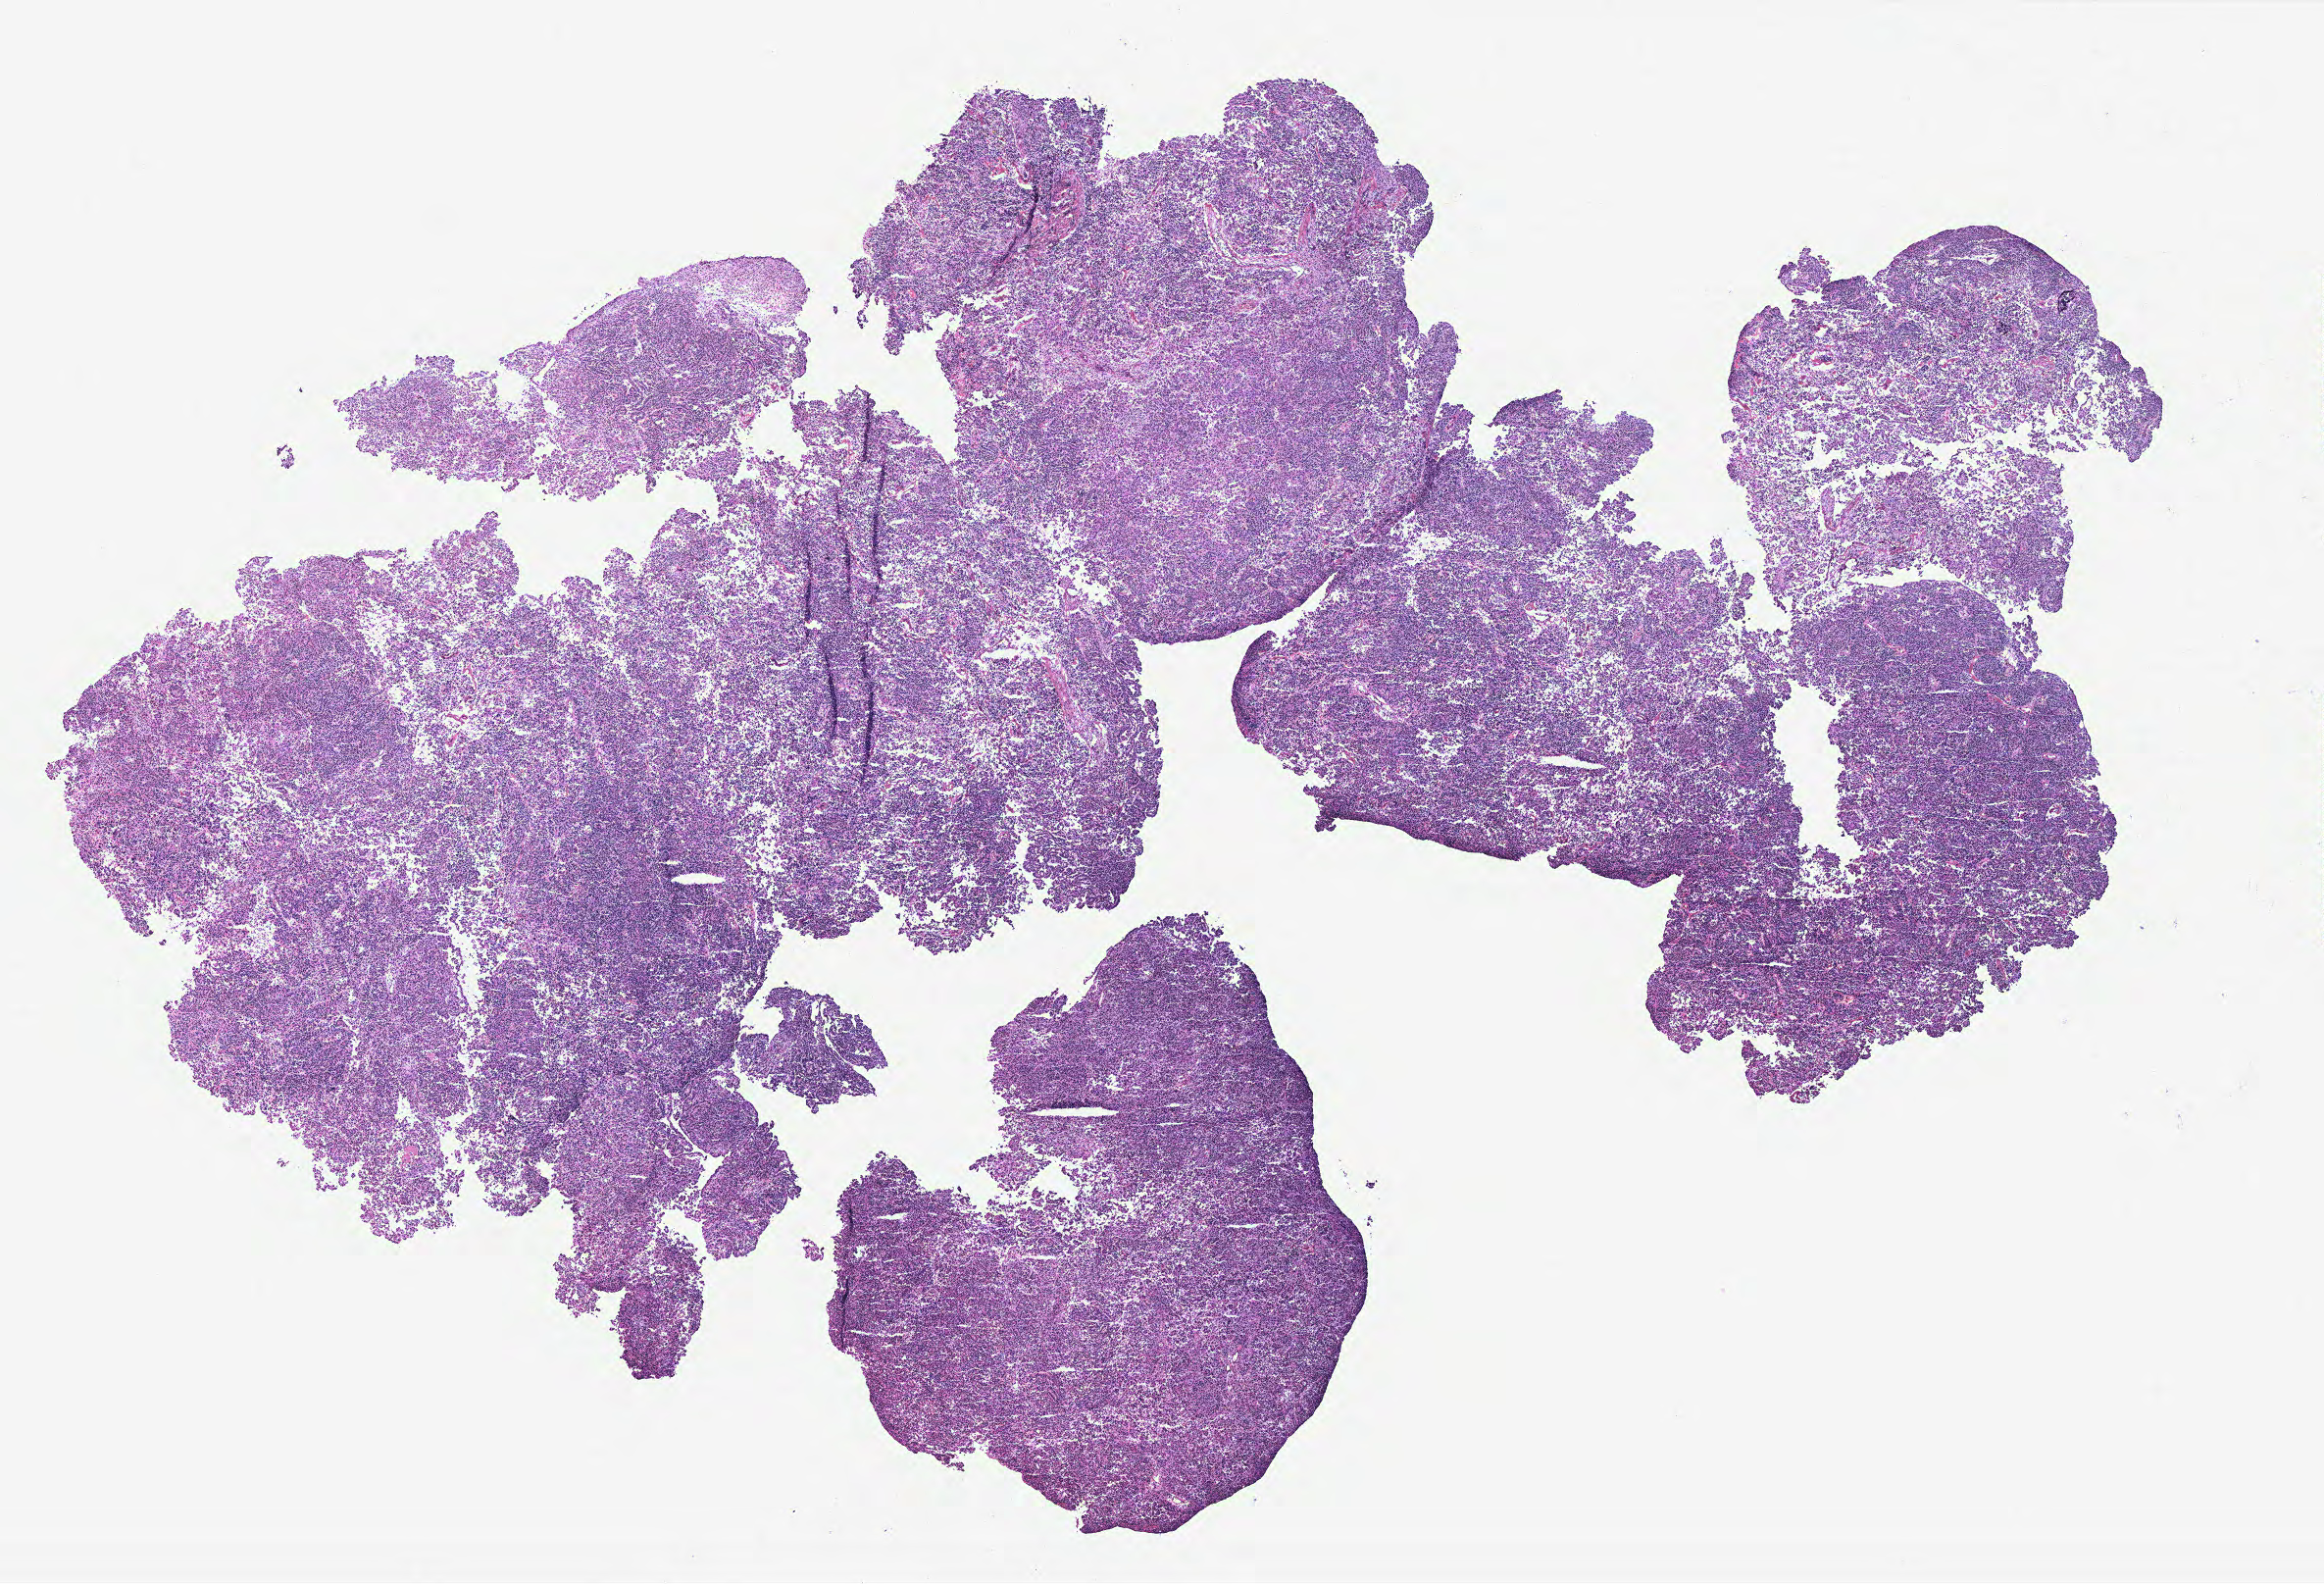
Hematoxylin and eosin (H&E) stained whole-slide image — shown as a low-resolution overview of the whole scanned area (about 19.0 x 12.9 mm, slide scanned at 40x), ovary, tumour tissue. Patient: female, age 79 years.
Diagnosis: Serous adenocarcinoma, NOS. Primary tumour site (as recorded): ovary.